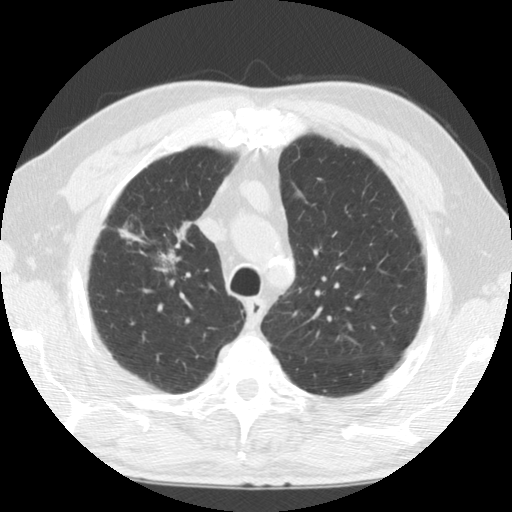
Chest CT (low-dose screening protocol), one axial image; baseline screening round; lung window (W 1500 / L -600 HU); 2.5 mm slice thickness; standard (soft-tissue) reconstruction kernel (STANDARD); slice 23 of 124 in the series; 512 × 512 image matrix, field of view 320 × 320 mm. Male participant, aged 69 years at enrolment.
Expert-annotated lung lesion, bounding box <101,203,203,292> (left, top, right, bottom; pixels). No non-calcified nodule or mass ≥4 mm was recorded by the screening reader at this exam. Official screen result: negative screen, minor abnormalities not suspicious for lung cancer. Later outcome: lung cancer diagnosed 171 days after this screen — adenocarcinoma, NOS, right upper lobe, poorly differentiated (G3), stage IIIB (AJCC 6th edition), 40 mm at pathology.